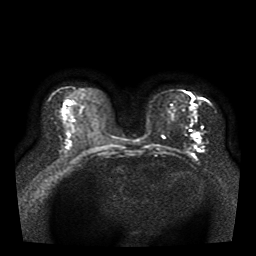
Breast MRI, one axial slice; slice 19 of 41 in the series (ordered by position); diffusion-weighted series; image 2 of 4 stored at this slice position (different b-values; order by instance number); 1.5 T; 5 mm slice thickness; 256 × 256 image matrix, field of view 330 × 330 mm. Female patient.
Annotated regions visible in this slice (expert manual segmentation):
- tumour on diffusion-weighted imaging: box from (x=197, y=141) to (x=201, y=143) px